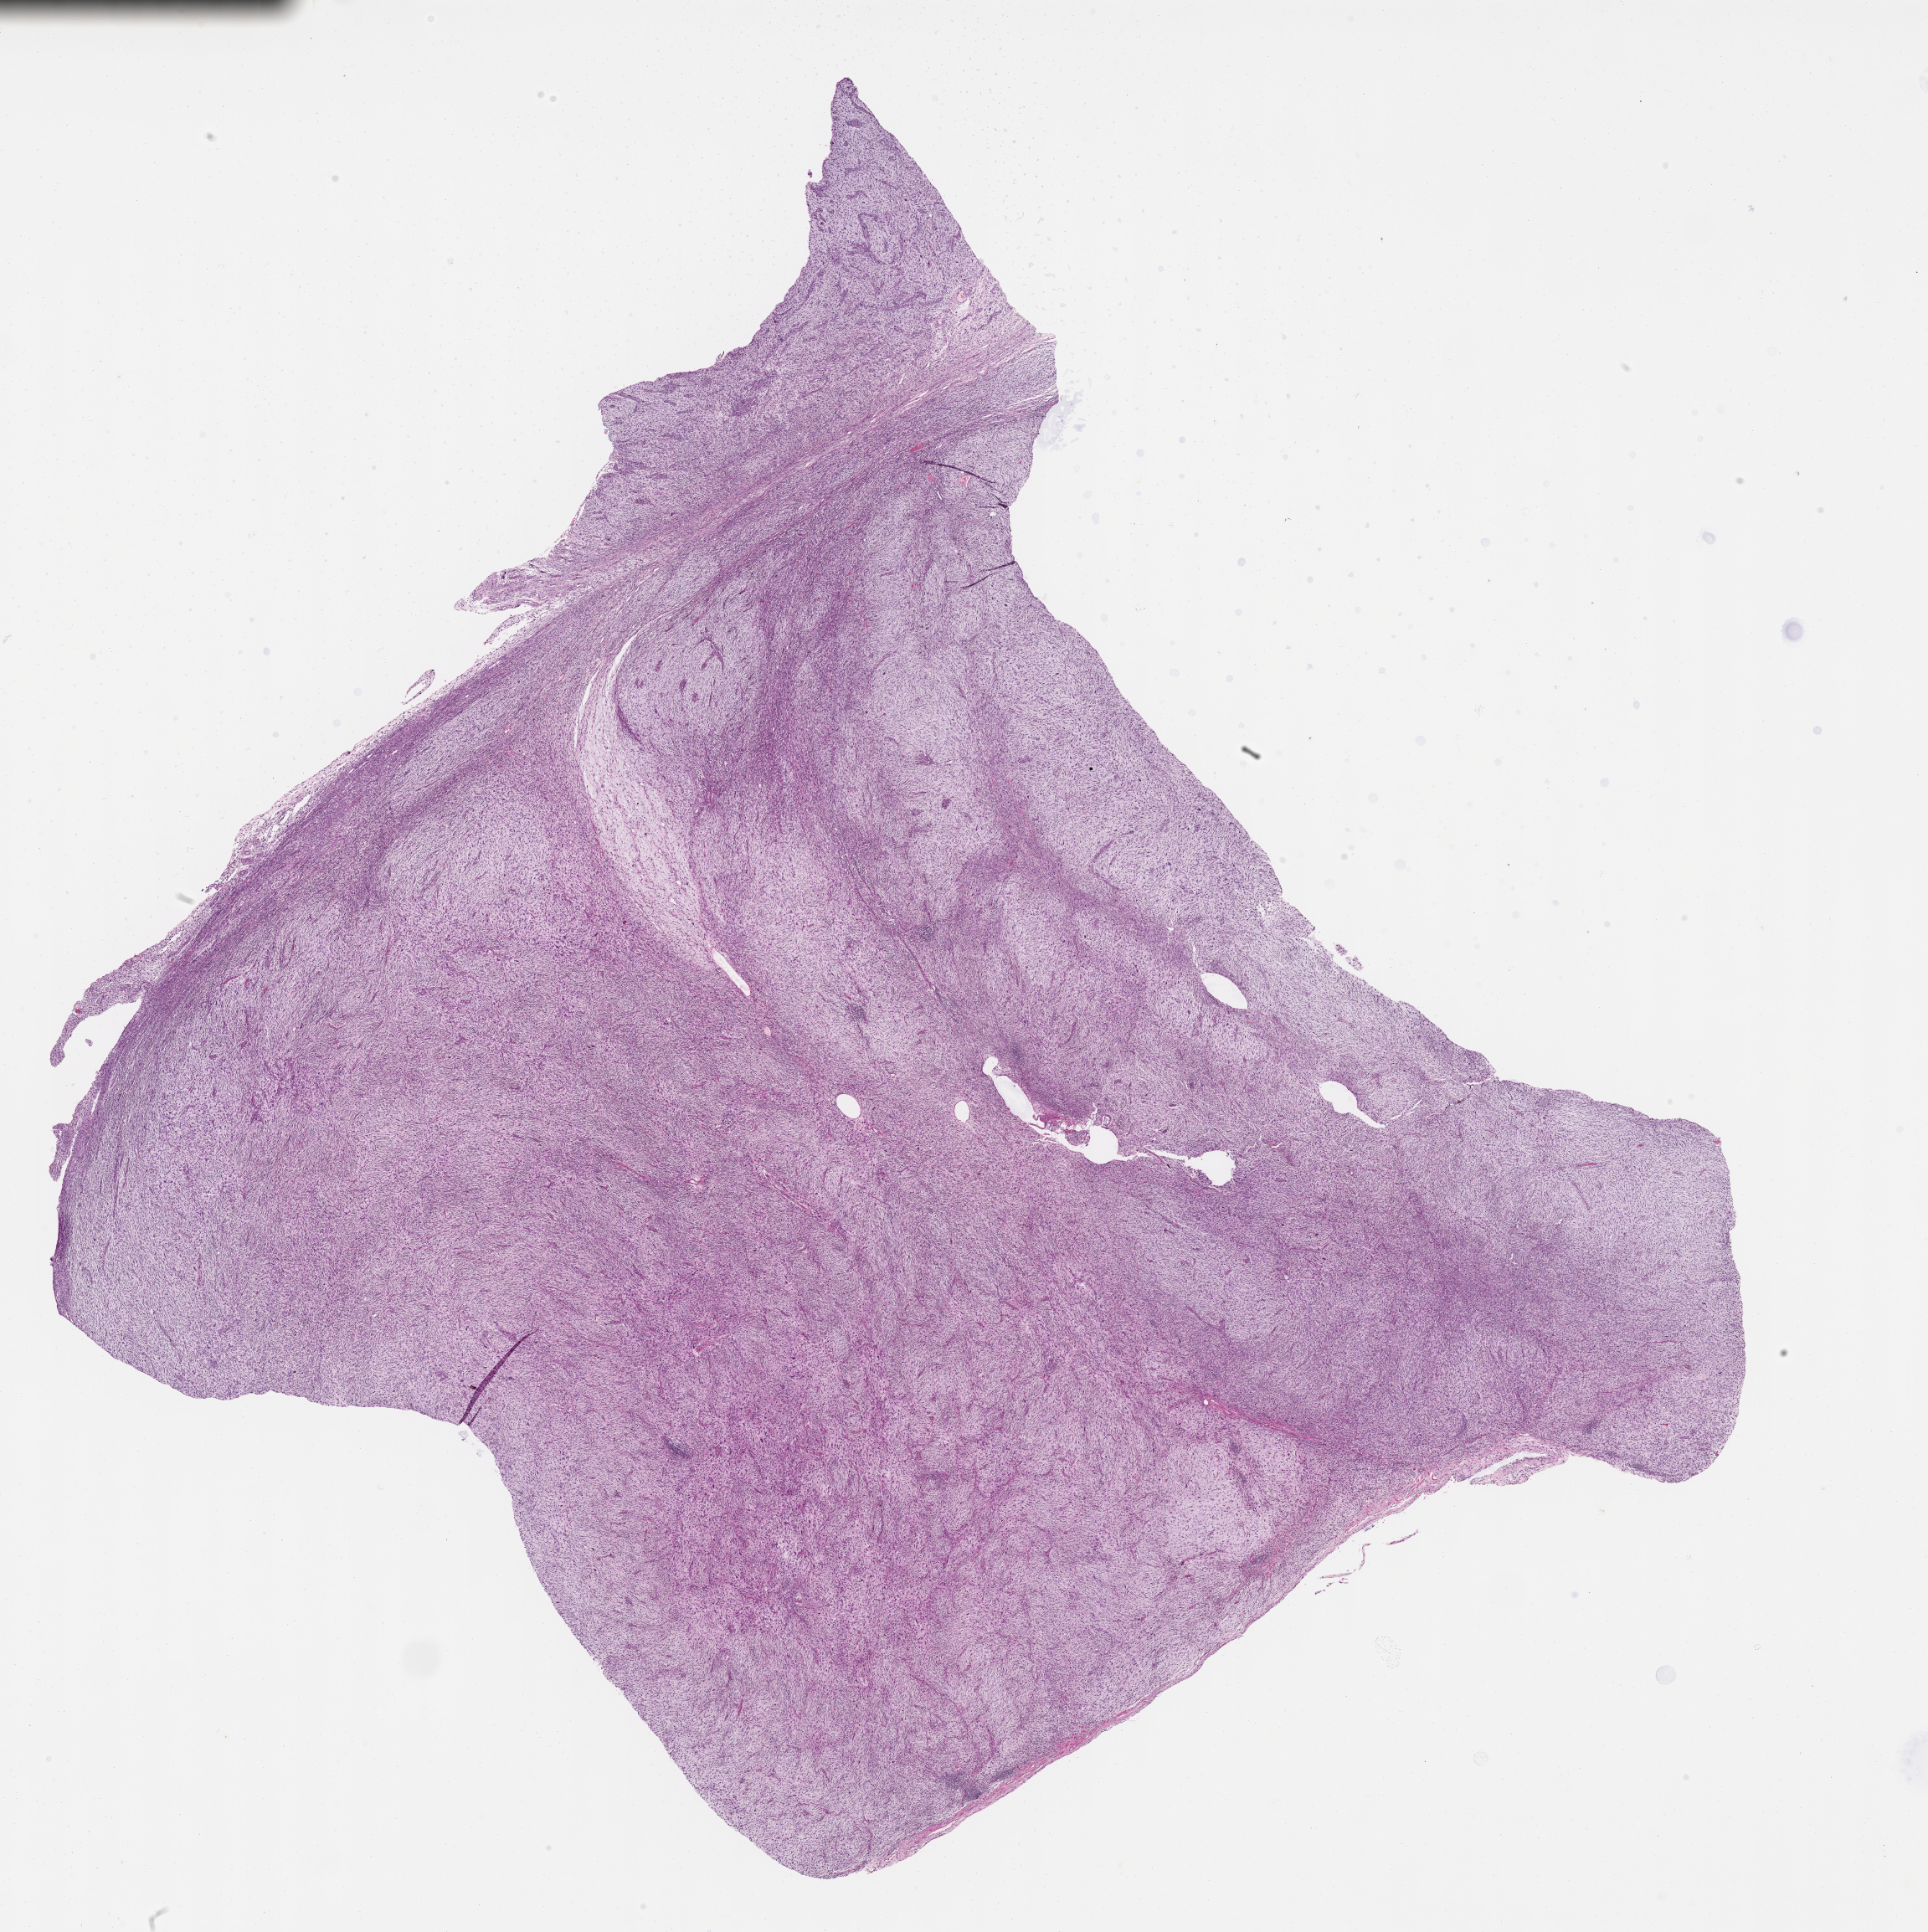
Digitized Hematoxylin and eosin (H&E) stained tissue section (whole slide) — low-resolution overview of the scanned area, about 18.6 x 18.7 mm, formalin-fixed paraffin-embedded (FFPE) diagnostic section, primary tumour sample from the connective, subcutaneous and other soft tissues. Patient: male, age at initial diagnosis 61 years.
Pathologic diagnosis: Fibromyxosarcoma (connective, subcutaneous and other soft tissues of pelvis).